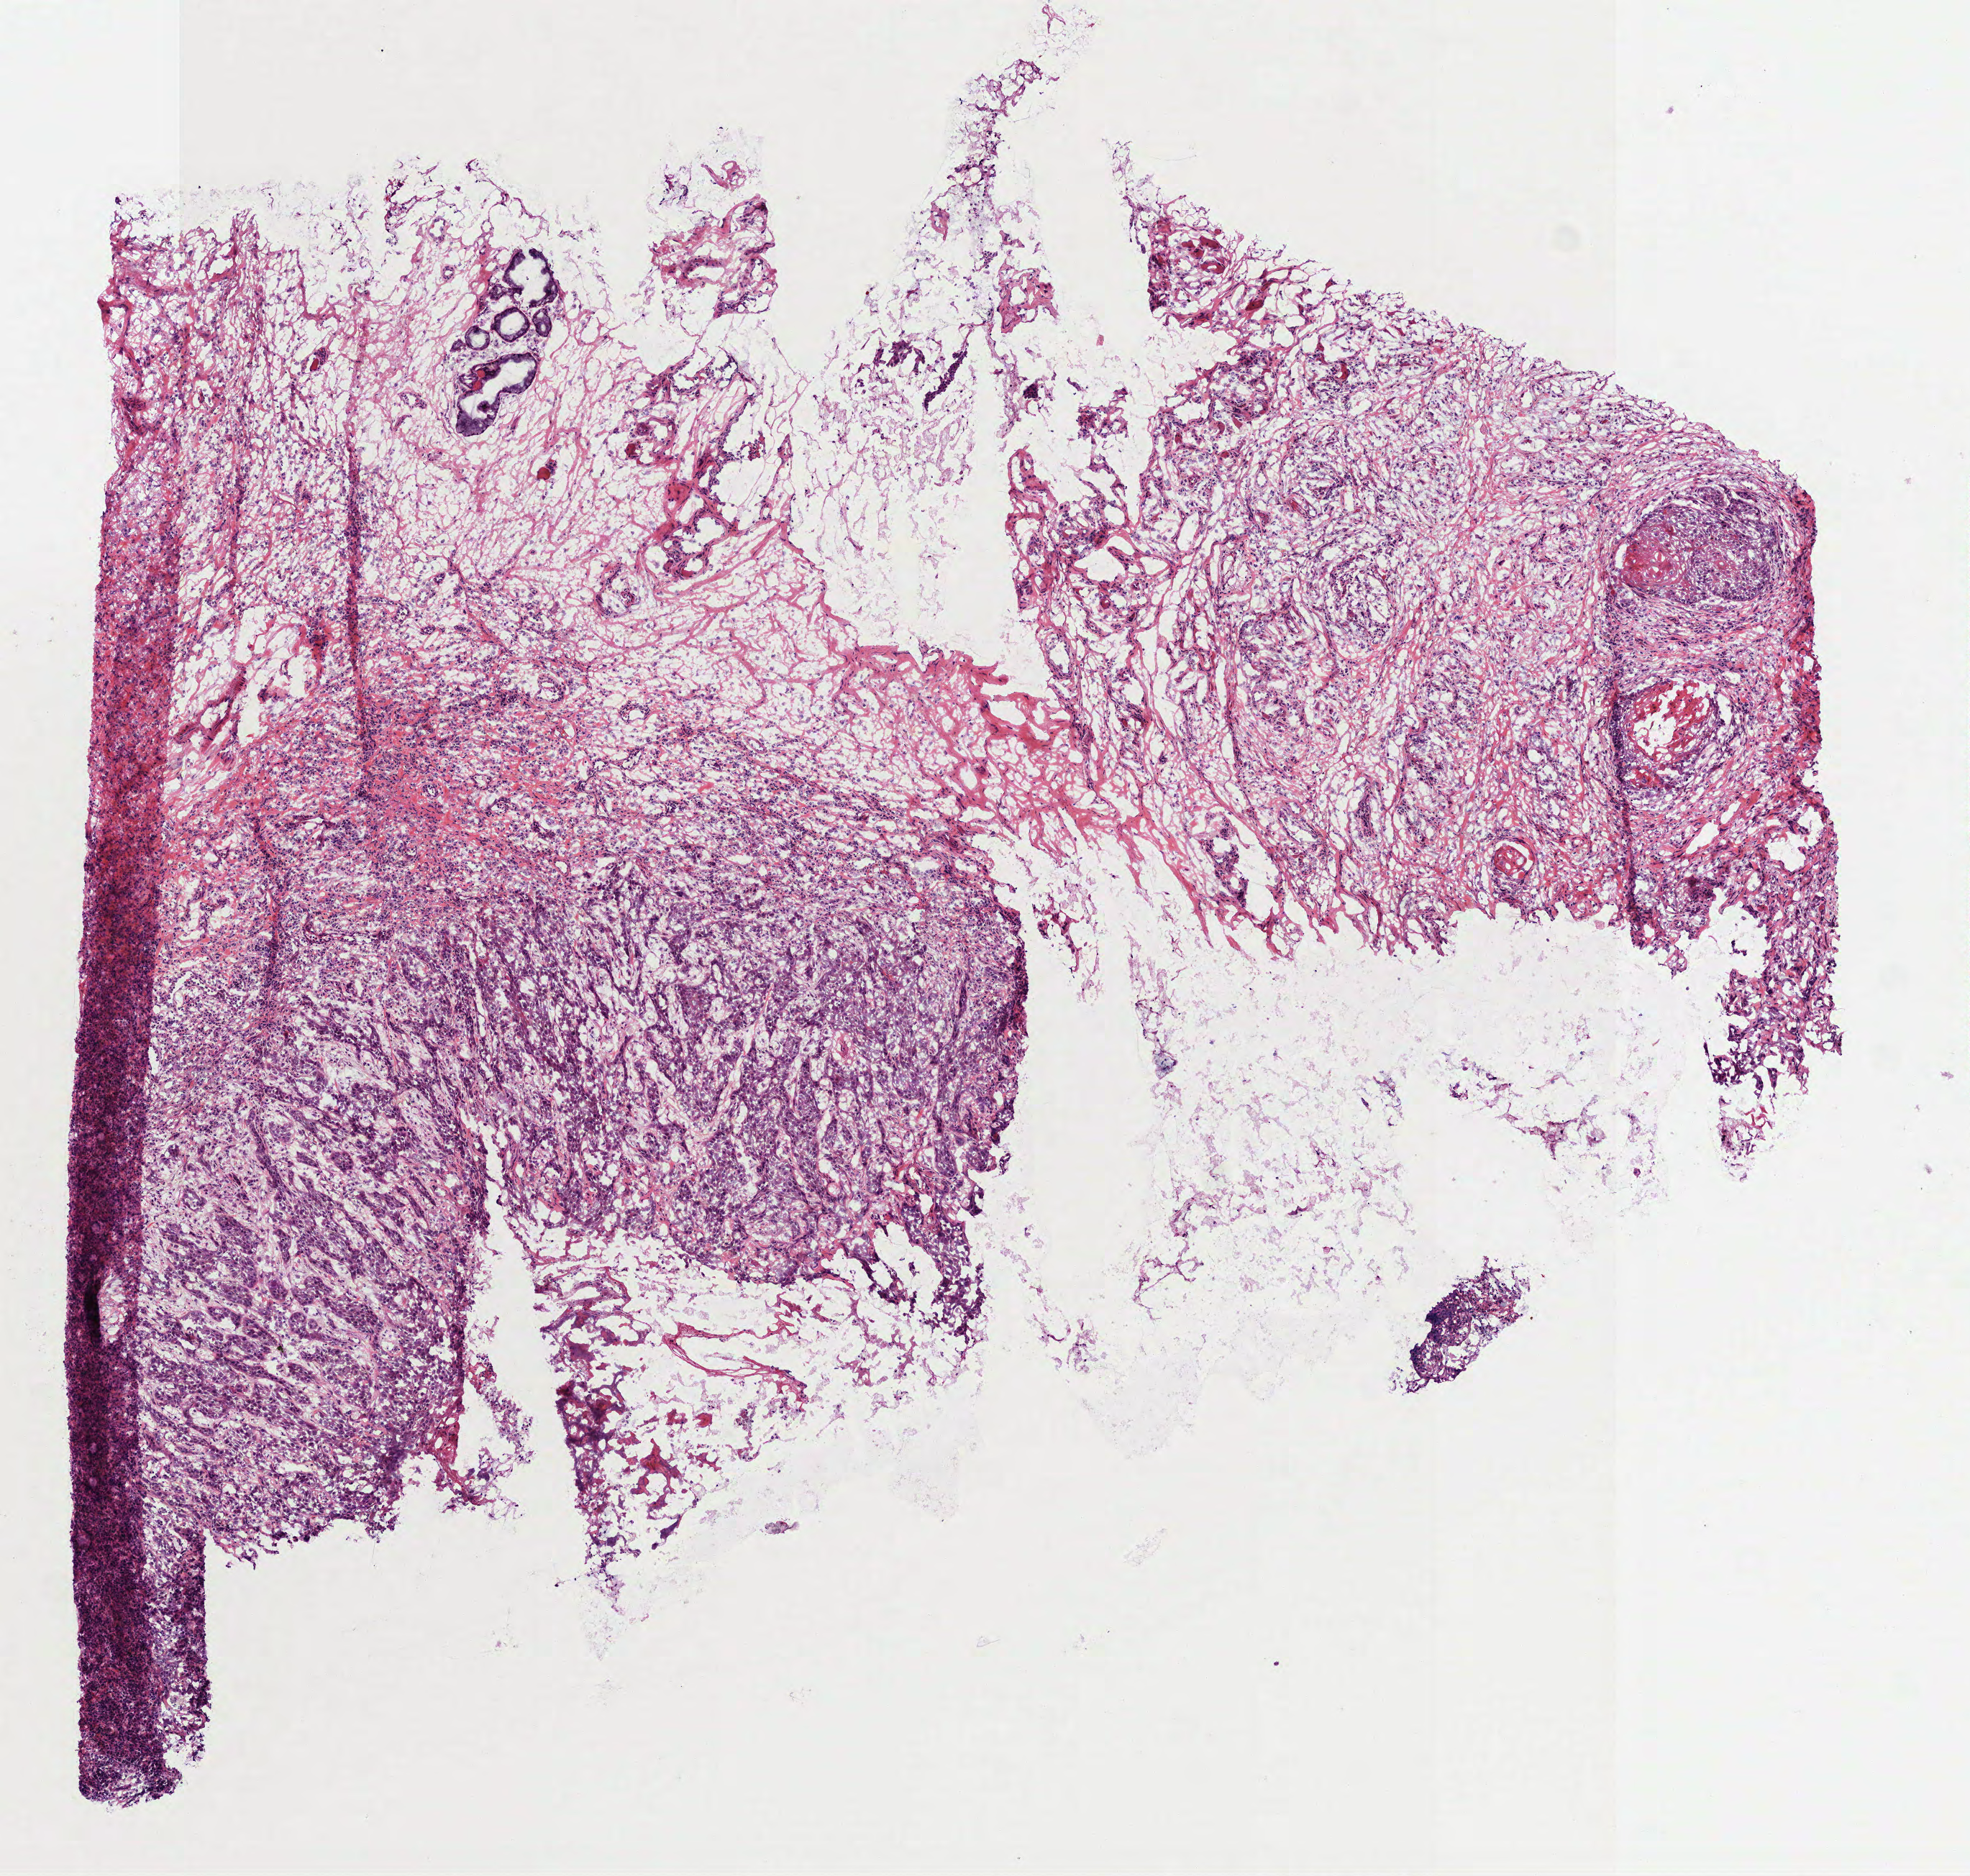
H&E-stained whole-slide image — a low-resolution overview of the entire scanned area, about 5.5 x 5.3 mm (from a 40x scan); frozen section from the top of the tissue portion; sample: primary tumour, head and neck. Patient: male, age at initial diagnosis 62 years. Histologic grade: G2 (moderately differentiated). Pathologist review of this section (percent, as recorded): tumour cells 40%, tumour nuclei 60%, normal cells 0%, stromal cells 60%, necrosis 0%. Inflammatory infiltration, as recorded: lymphocyte infiltration 25%, monocyte infiltration 0%, neutrophil infiltration 10%.
- TNM: T2 N0 M0
- AJCC pathologic stage: II (7th edition)
- laterality: left
- histologic diagnosis: Squamous cell carcinoma, keratinizing, NOS (larynx, NOS)